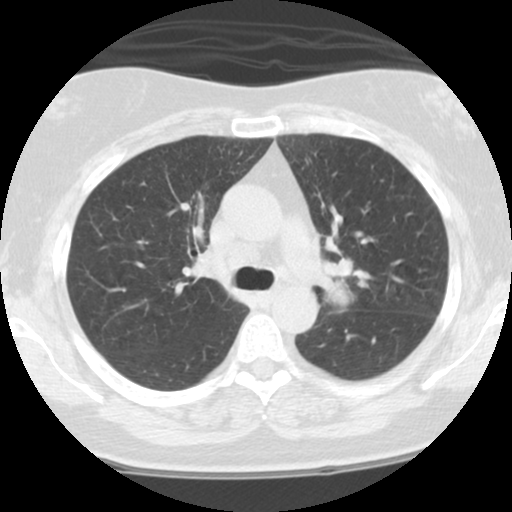
Low-dose screening chest CT, one axial slice. Slice 74 of 108 in the series (ordered by position). Reconstruction kernel STANDARD. 120 kVp. Lung window (W 1500 / L -600 HU). 2.5 mm slice thickness. 512 × 512 image matrix, field of view 300 × 300 mm.
Outlined on this slice (outlined manually by an expert reader):
- lesion 1 (tumor, hilum of left lung): bounding box (x1, y1, x2, y2) in pixels: (329, 282, 349, 305)